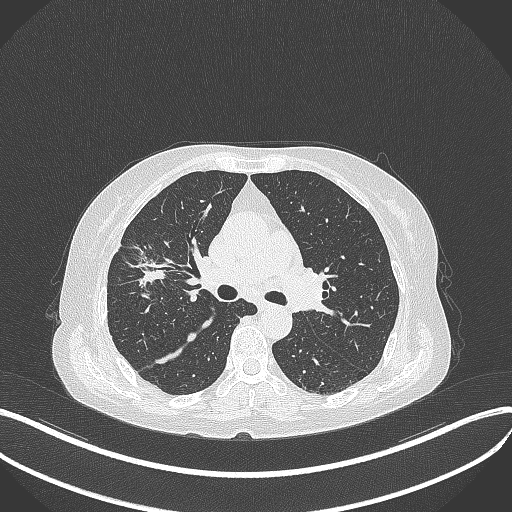
Chest CT, one axial slice. Position 245 of 429 along the scan axis. Lung window (W 1500 / L -600 HU). 512 × 512 image matrix, field of view 400 × 400 mm. Patient: female, 69 years. Case-level facts recorded for this patient, not image findings: clinical TNM (as recorded): T1b N3 M0.
Outlined on this slice (rectangle marked by the reading radiologist):
- lung tumour (recorded histology: small cell carcinoma): bounding box (x1, y1, x2, y2) in pixels: (123, 246, 170, 286)